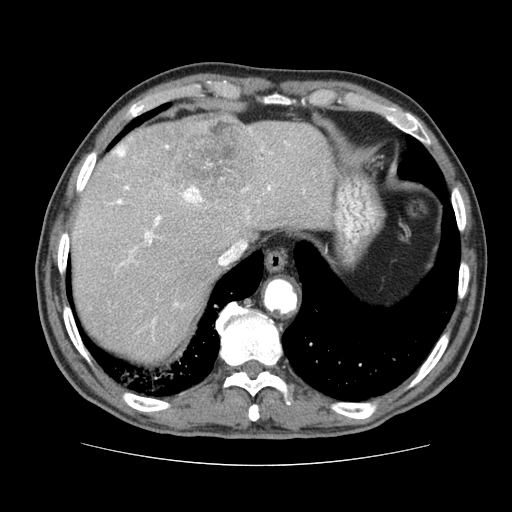
Contrast-enhanced abdominal CT (liver protocol), one axial slice. Position 62 of 79 along the scan axis. 120 kVp. Soft-tissue window (W 400 / L 40 HU). 2.5 mm slice thickness. 512 × 512 image matrix, field of view 360 × 360 mm. From the clinical record (not read from this slice): diagnosis: hepatocellular carcinoma (patient treated with transarterial chemoembolisation; whether this scan precedes or follows treatment is not stated here); TNM stage (as recorded): Stage-I; Child-Pugh class: A; tumour nodularity: uninodular.
Structures marked on this image (semi-automatic segmentation, software-assisted and operator-edited):
- liver parenchyma outside the tumour (the mass and vessels are separate outlines, so this box may not span the whole liver): bounding box [x1, y1, x2, y2] px = [70, 114, 334, 361]
- mass: [147, 116, 259, 204]
- liver vessels: [111, 142, 305, 323]